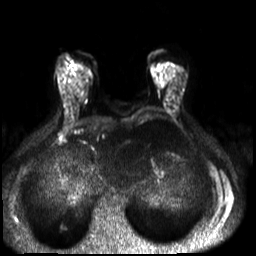
Breast MRI, one axial slice. Position 10 of 30 along the scan axis. Diffusion-weighted series; image 2 of 4 stored at this slice position (different b-values; order by instance number). 3 T. 4 mm slice thickness. 256 × 256 image matrix, field of view 320 × 320 mm. Female patient.
Outlined on this slice (expert manual segmentation):
- tumour on diffusion-weighted imaging: box from (x=87, y=70) to (x=92, y=76) px